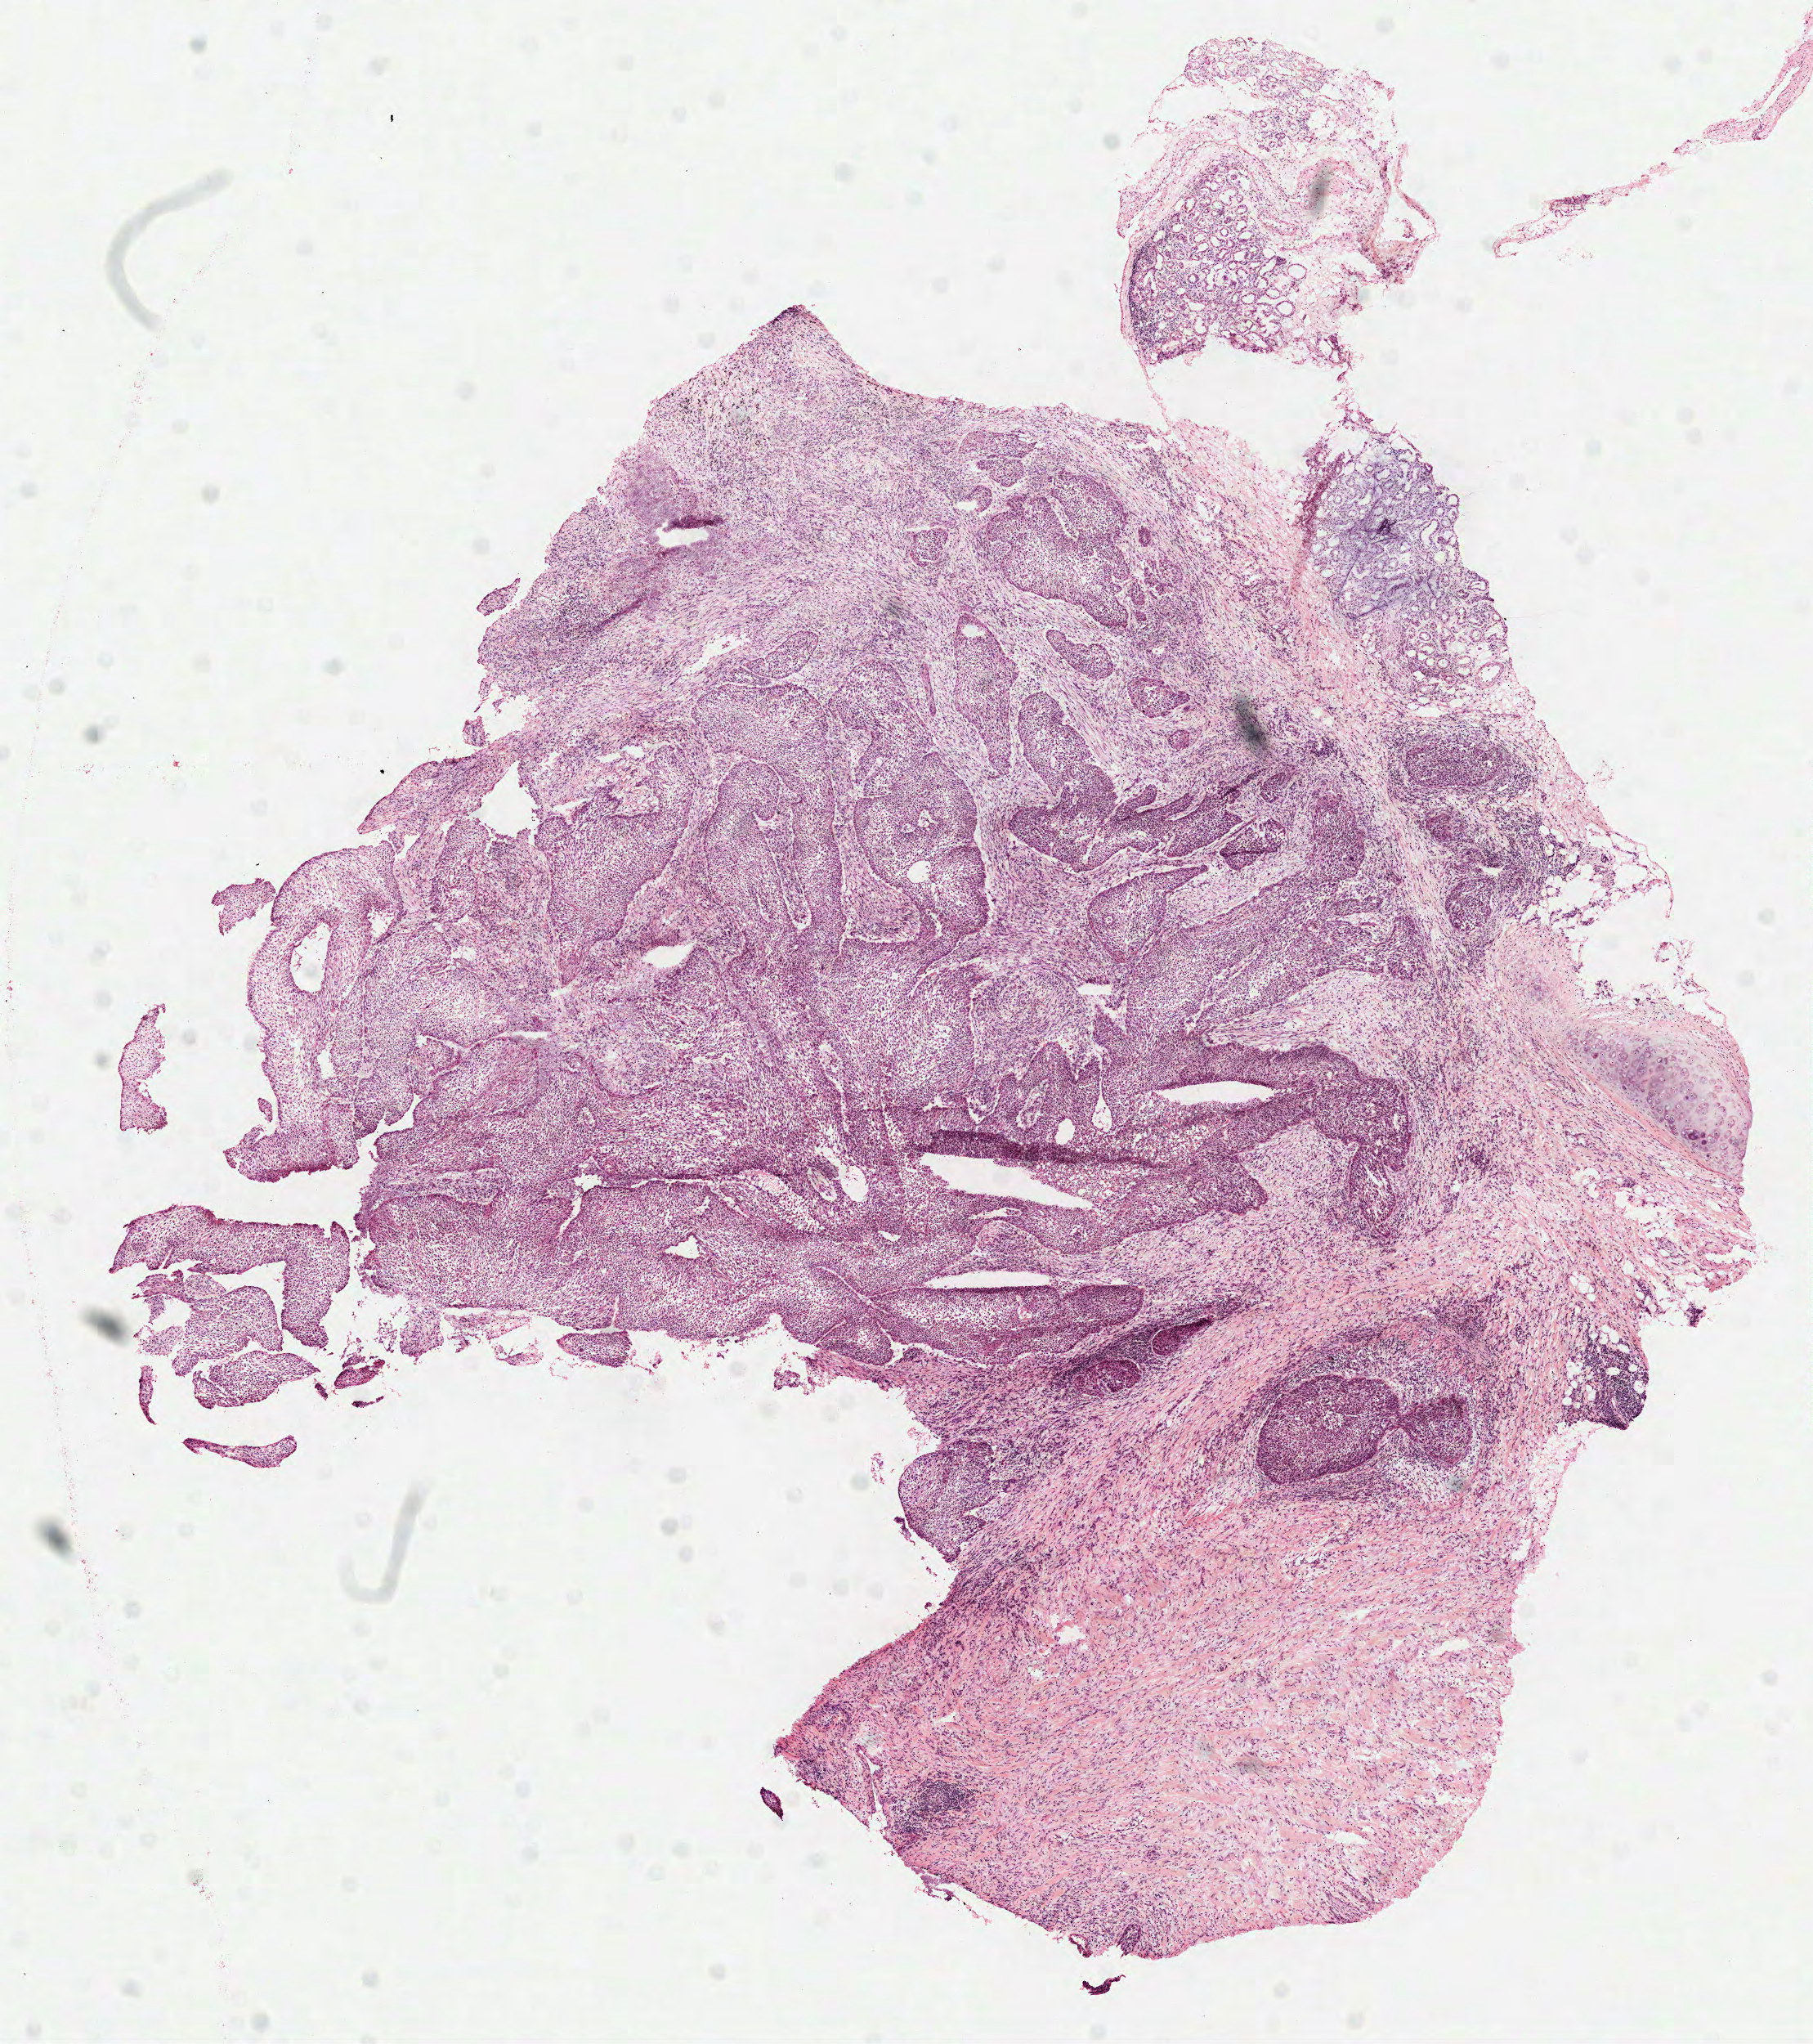
Digitized Hematoxylin and eosin (H&E) stained tissue section (whole slide), a low-resolution overview of the entire scanned area, about 8.9 x 10.1 mm (acquisition: 40x scan); frozen section from the top of the tissue portion; lung, primary tumour sample. Patient: male, age at initial diagnosis 83 years. Pathologist review of this section (percent, as recorded): tumour cells 60%, tumour nuclei 60%, normal cells 5%, stromal cells 33%, necrosis 2%. Inflammatory infiltration, as recorded: lymphocyte infiltration 20%.
Diagnosis: Squamous cell carcinoma, NOS (lower lobe, lung). AJCC pathologic stage: IIB. Laterality: left.